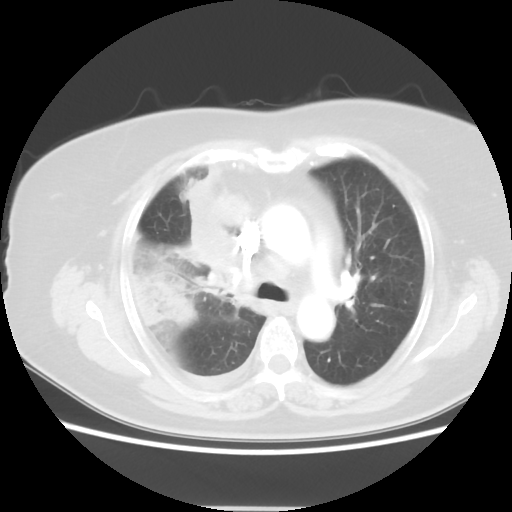
Chest CT, one axial slice. Position 32 of 48 along the scan axis. Reconstruction kernel STANDARD. 120 kVp. Lung window (W 1500 / L -600 HU). 5 mm slice thickness. 512 × 512 image matrix. Female patient, age 73 years. Case-level facts recorded for this patient, not image findings: clinical TNM (as recorded): T3 N3 M1b.
Structures marked on this image (rectangle marked by the reading radiologist):
- lung tumour (recorded histology: small cell carcinoma): bounding box <182,177,250,286> (left, top, right, bottom; pixels)